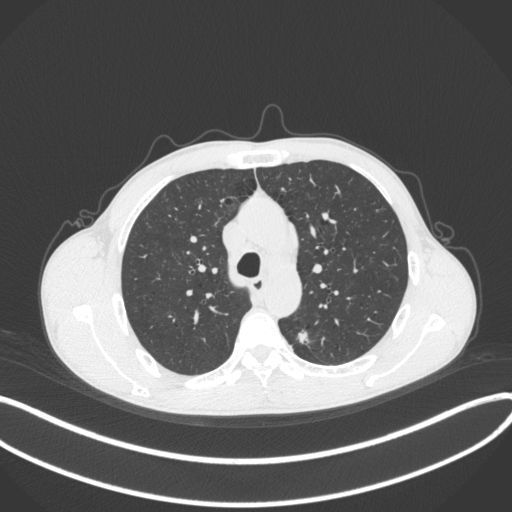
Chest CT, one axial slice; position 279 of 429 along the scan axis; reconstruction kernel B31f; lung window (W 1500 / L -600 HU); 1 mm slice thickness; 512 × 512 image matrix. Patient: male, 51 years. Case-level facts recorded for this patient, not image findings: clinical TNM (as recorded): T2a N1 M1.
Outlined on this slice (rectangle marked by the reading radiologist):
- lung tumour (recorded histology: adenocarcinoma): bounding box <294,325,313,350> (left, top, right, bottom; pixels)